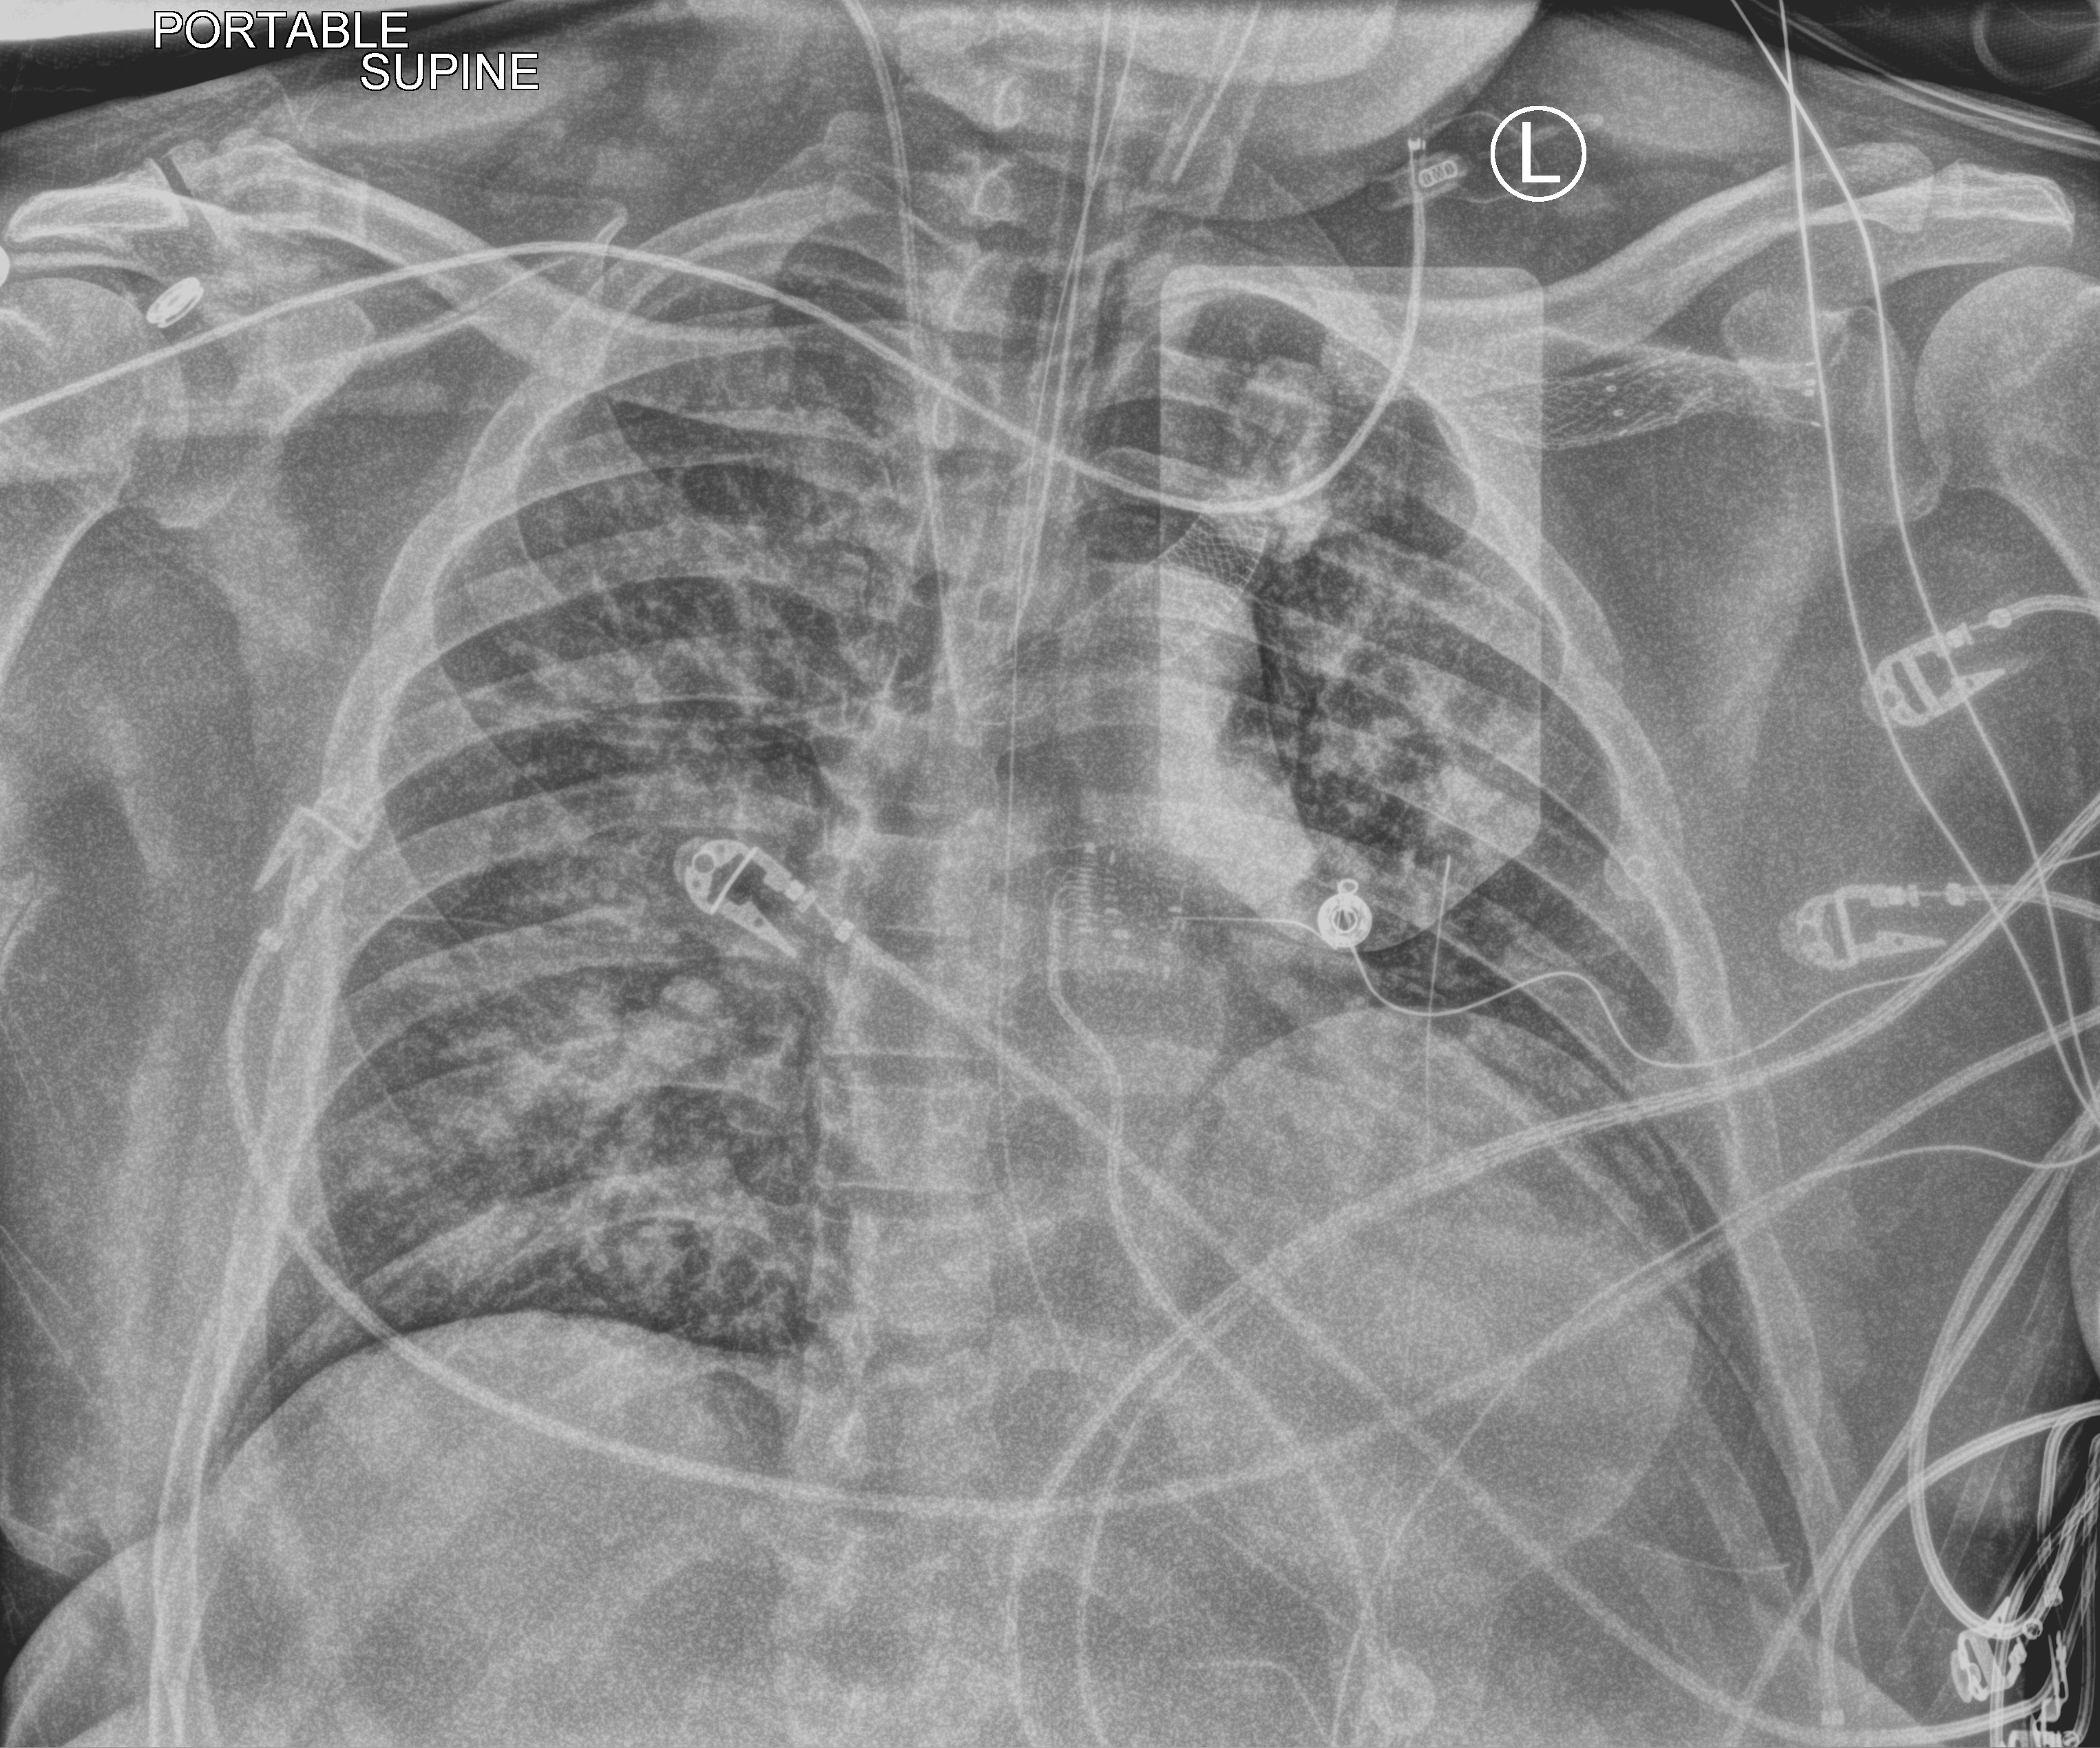
Portable chest radiograph; anteroposterior (AP) projection. Male patient hospitalised with COVID-19, age 18–59 years.
Admission-level facts for this patient (not findings on this image; timing relative to this image not recorded):
- length of hospital stay: 41 days
- admitted to intensive care during this hospital stay: yes